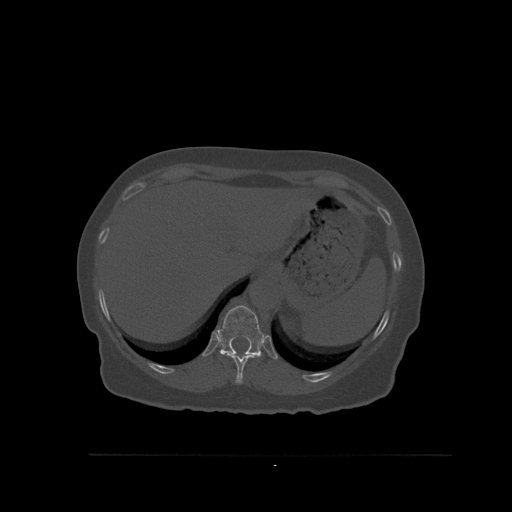
CT including the spine, one axial slice; slice 309 of 527 in the series (ordered by position); bone window (W 1800 / L 400 HU); 1.5 mm slice thickness; 512 × 512 image matrix. Female patient, age 73 years. Case-level facts recorded for this patient, not image findings: primary cancer: breast.
Outlined on this slice (semi-automatic segmentation, software-assisted and operator-edited):
- T10 vertebra: box from (x=220, y=353) to (x=260, y=384) px
- T11 vertebra: (x=217, y=305)–(x=265, y=356)